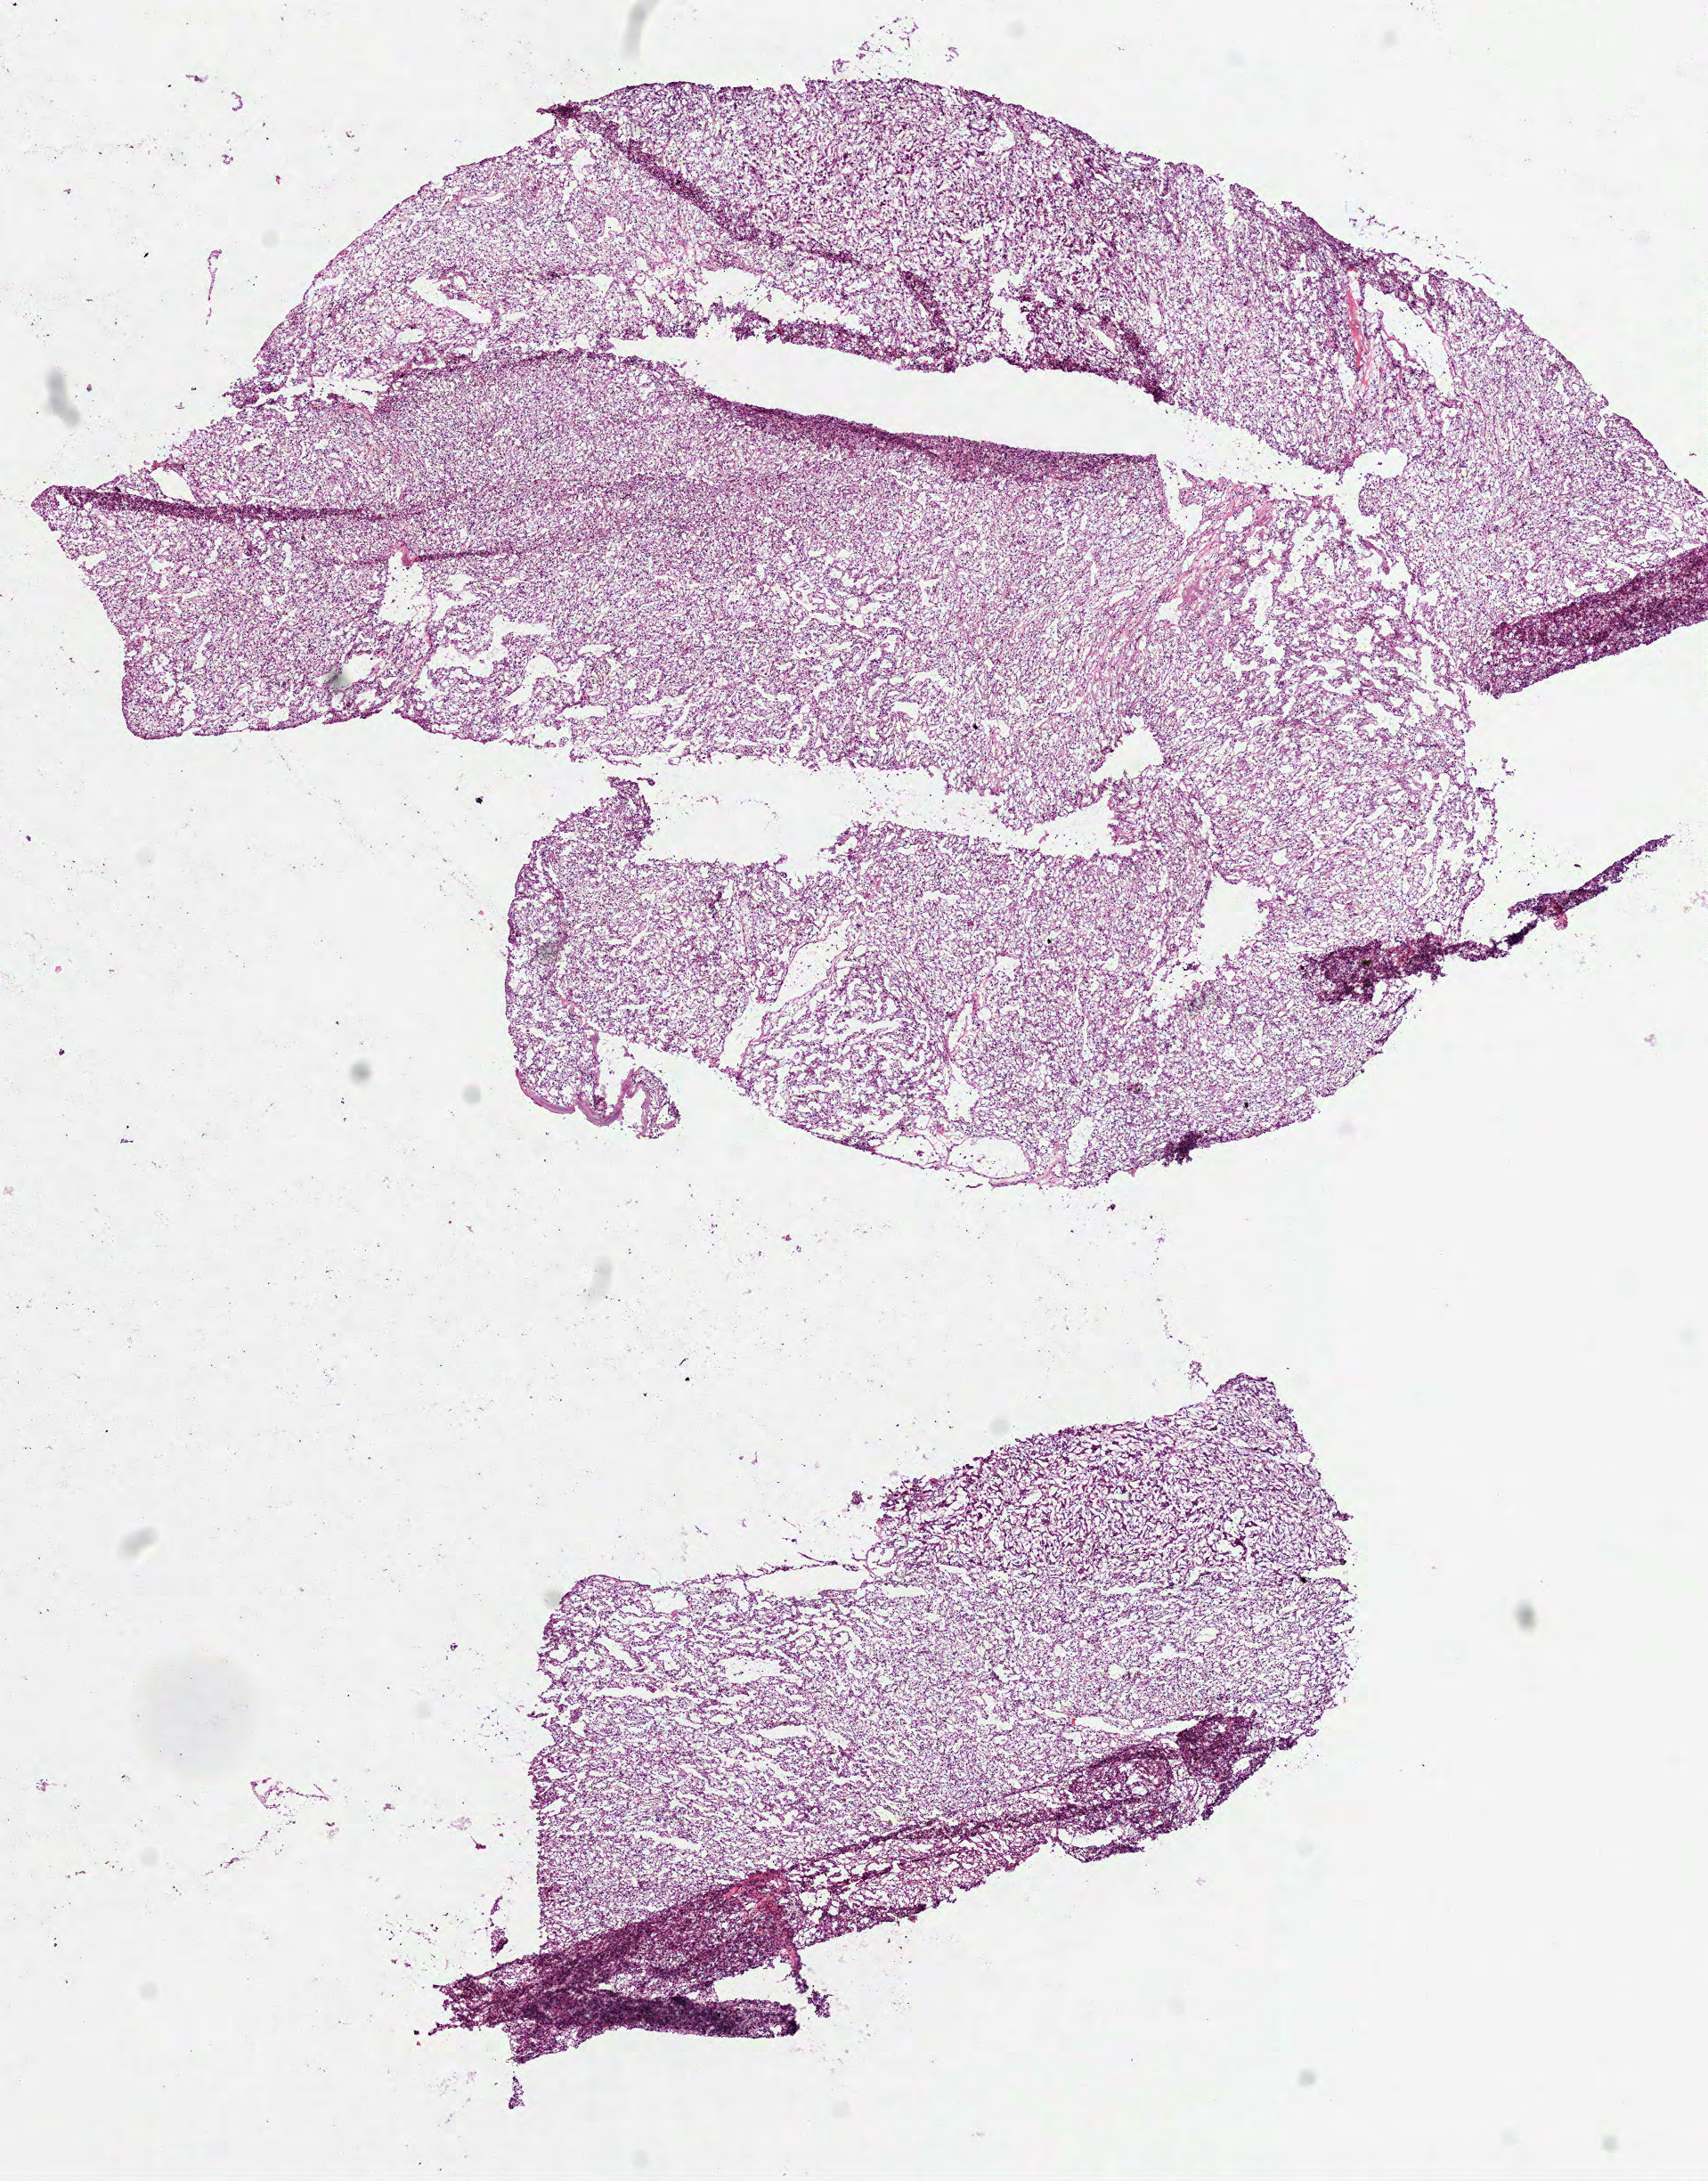
Digitized H&E-stained tissue section (whole slide) — a low-resolution overview of the entire scanned area, about 7.7 x 9.9 mm (acquisition: 40x scan). Frozen section from the top of the tissue portion. Kidney, primary tumour sample. Male patient; age at initial diagnosis 74 years. Histologic grade: G3 (poorly differentiated). Composition of this section per pathologist review: tumour cells 95%, tumour nuclei 85%, normal cells 0%, stromal cells 5%, necrosis 0%.
Diagnosis: Clear cell adenocarcinoma, NOS. TNM: T3a NX M0. AJCC pathologic stage: III.